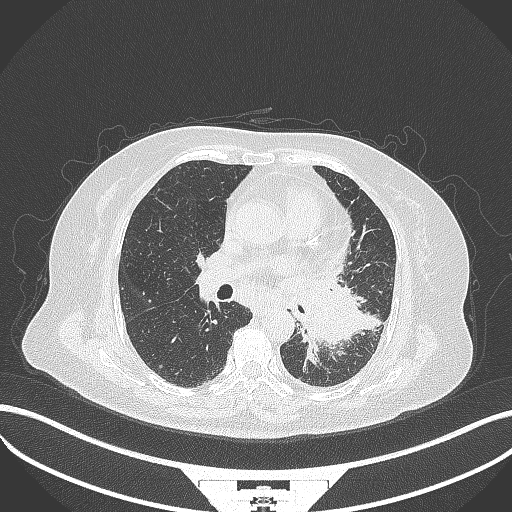
Chest CT, one axial slice. Position 184 of 322 along the scan axis. 120 kVp. Lung window (W 1500 / L -600 HU). 1 mm slice thickness. 512 × 512 image matrix, field of view 400 × 400 mm. Female patient, age 69 years. Case-level facts recorded for this patient, not image findings: clinical TNM (as recorded): T2b N3 M1.
Structures marked on this image (rectangle marked by the reading radiologist):
- lung tumour (recorded histology: adenocarcinoma): box from (x=298, y=283) to (x=367, y=350) px